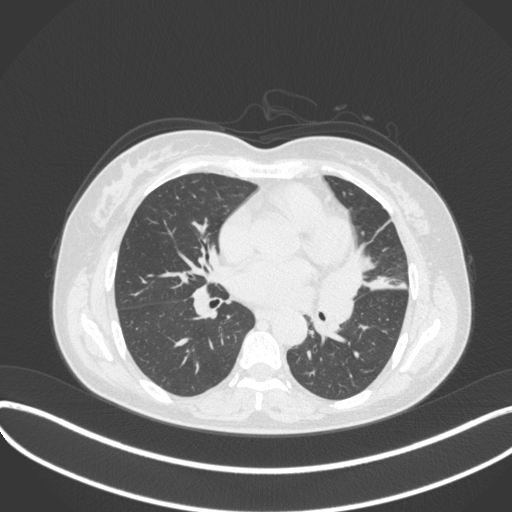
Chest CT, one axial slice. Position 173 of 373 along the scan axis. Reconstruction kernel B31f. Lung window (W 1500 / L -600 HU). 1 mm slice thickness. 512 × 512 image matrix, field of view 400 × 400 mm. Female patient, age 54 years. Case-level facts recorded for this patient, not image findings: clinical TNM (as recorded): T2a N1 M0.
Annotated regions visible in this slice (bounding box drawn by a radiologist):
- lung tumour (recorded histology: small cell carcinoma): bounding box (x1, y1, x2, y2) in pixels: (313, 240, 369, 346)